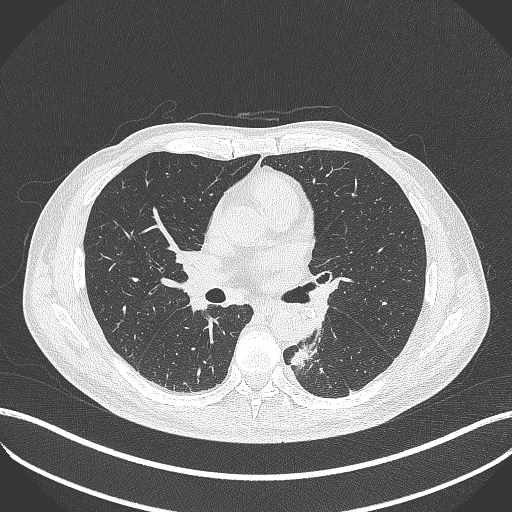
Chest CT, one axial slice; lung window (W 1500 / L -600 HU); 1 mm slice thickness; 512 × 512 image matrix, field of view 400 × 400 mm. Male patient, age 72 years. Case-level facts recorded for this patient, not image findings: clinical TNM (as recorded): T2b N0 M1.
Outlined on this slice (bounding box drawn by a radiologist):
- lung tumour (recorded histology: adenocarcinoma): bounding box (x1, y1, x2, y2) in pixels: (283, 321, 328, 368)